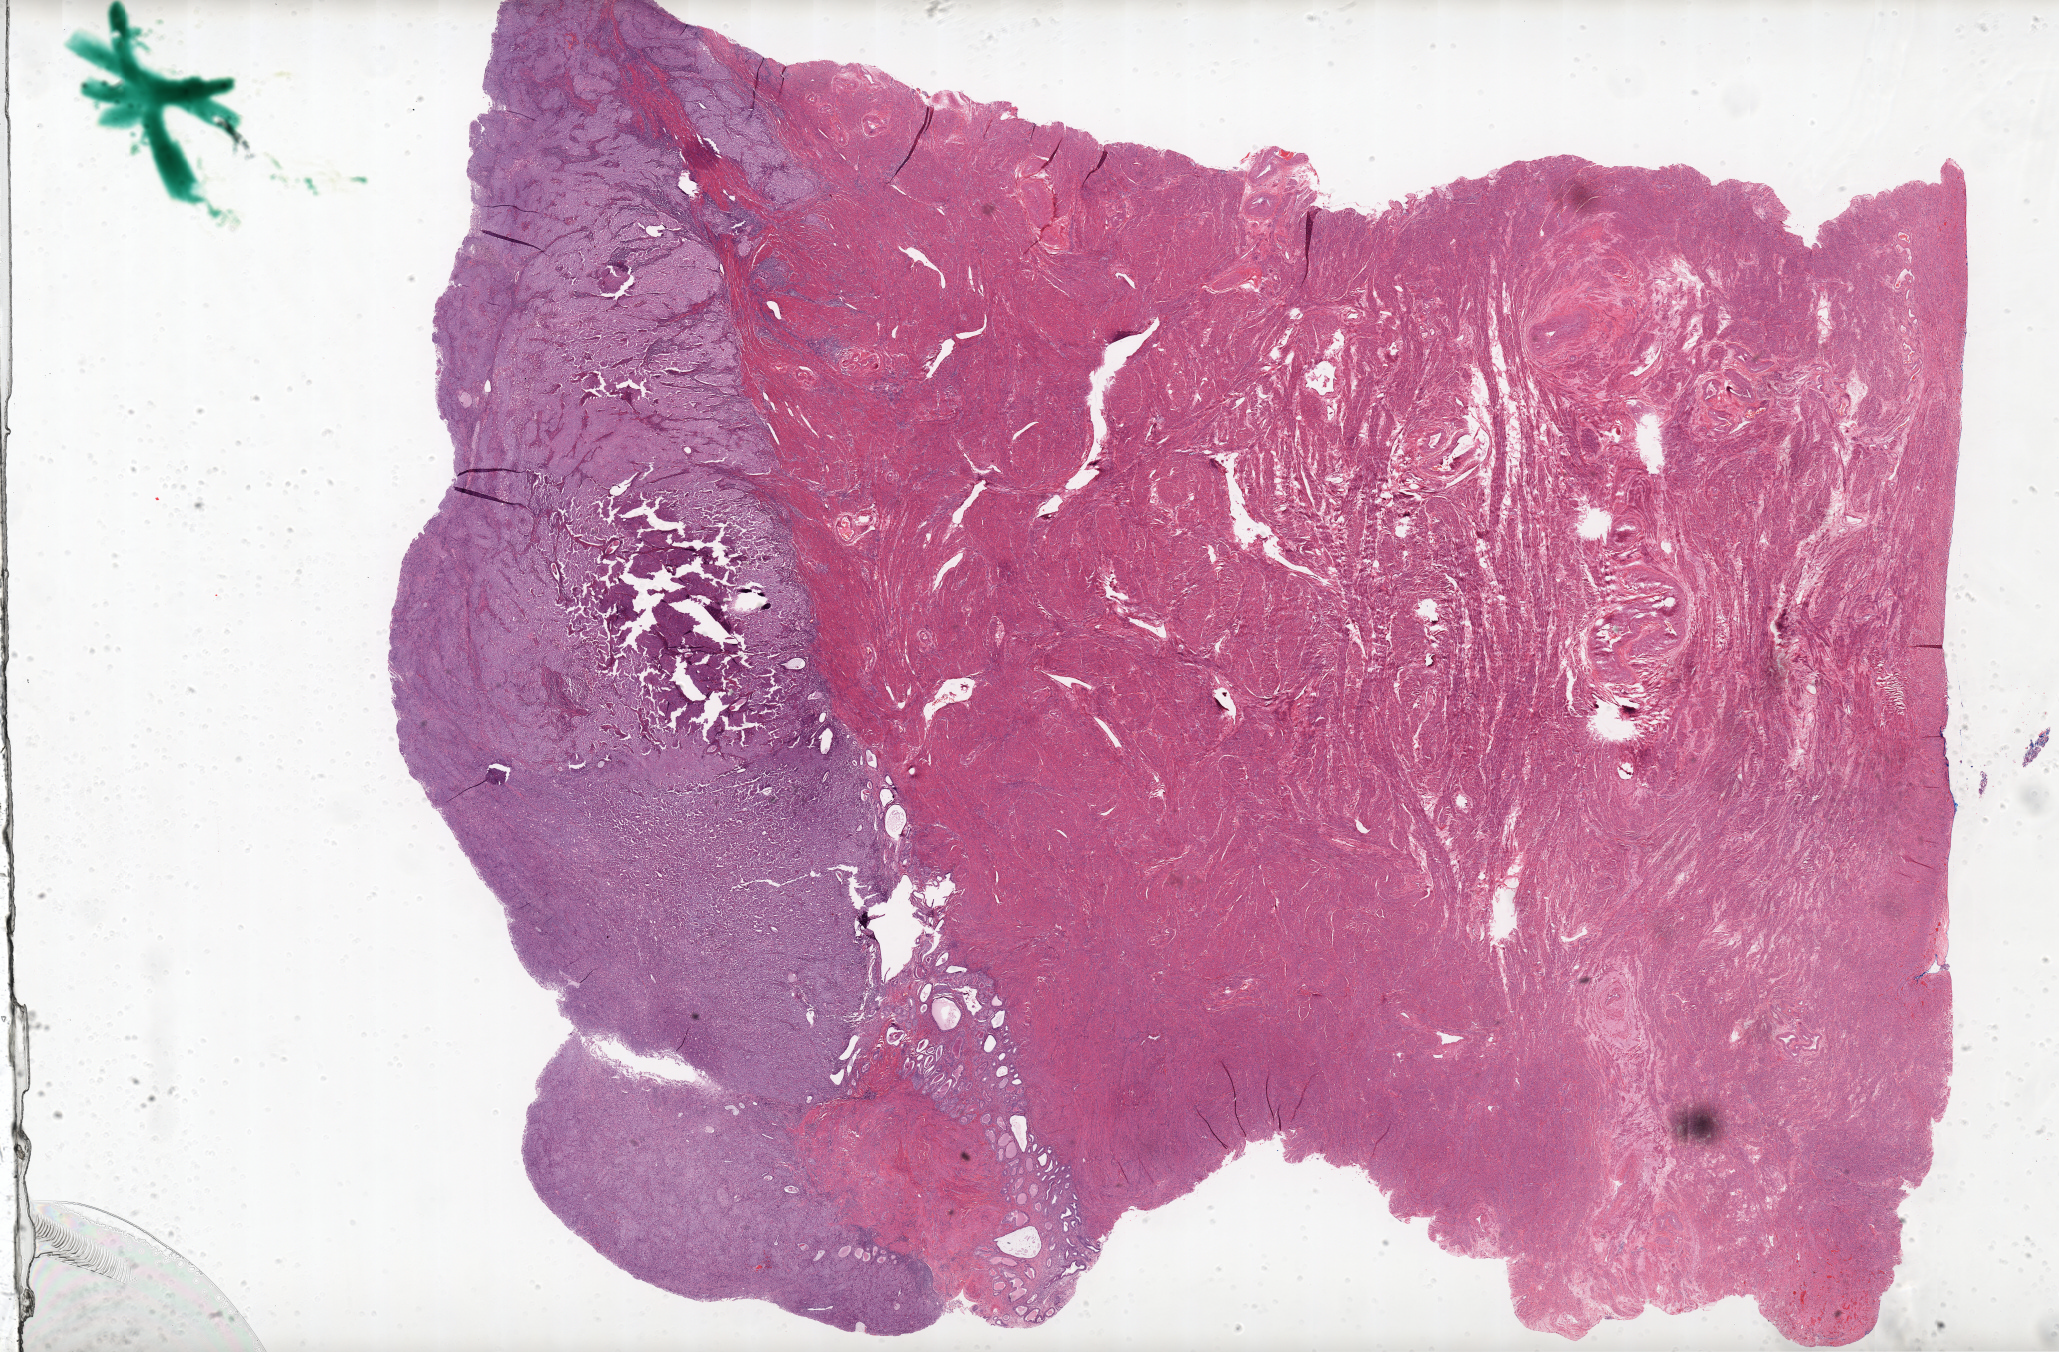
Whole-slide histology image, Hematoxylin and eosin (H&E) stained — a low-resolution overview of the entire scanned area, about 32.8 x 21.5 mm (acquisition: 20x scan). Formalin-fixed paraffin-embedded (FFPE) diagnostic section. Primary tumour sample from the uterus. Female, age 69 years at initial diagnosis. Histologic grade: G3 (poorly differentiated).
FIGO stage: IA. Diagnosis: Endometrioid adenocarcinoma, NOS (endometrium).